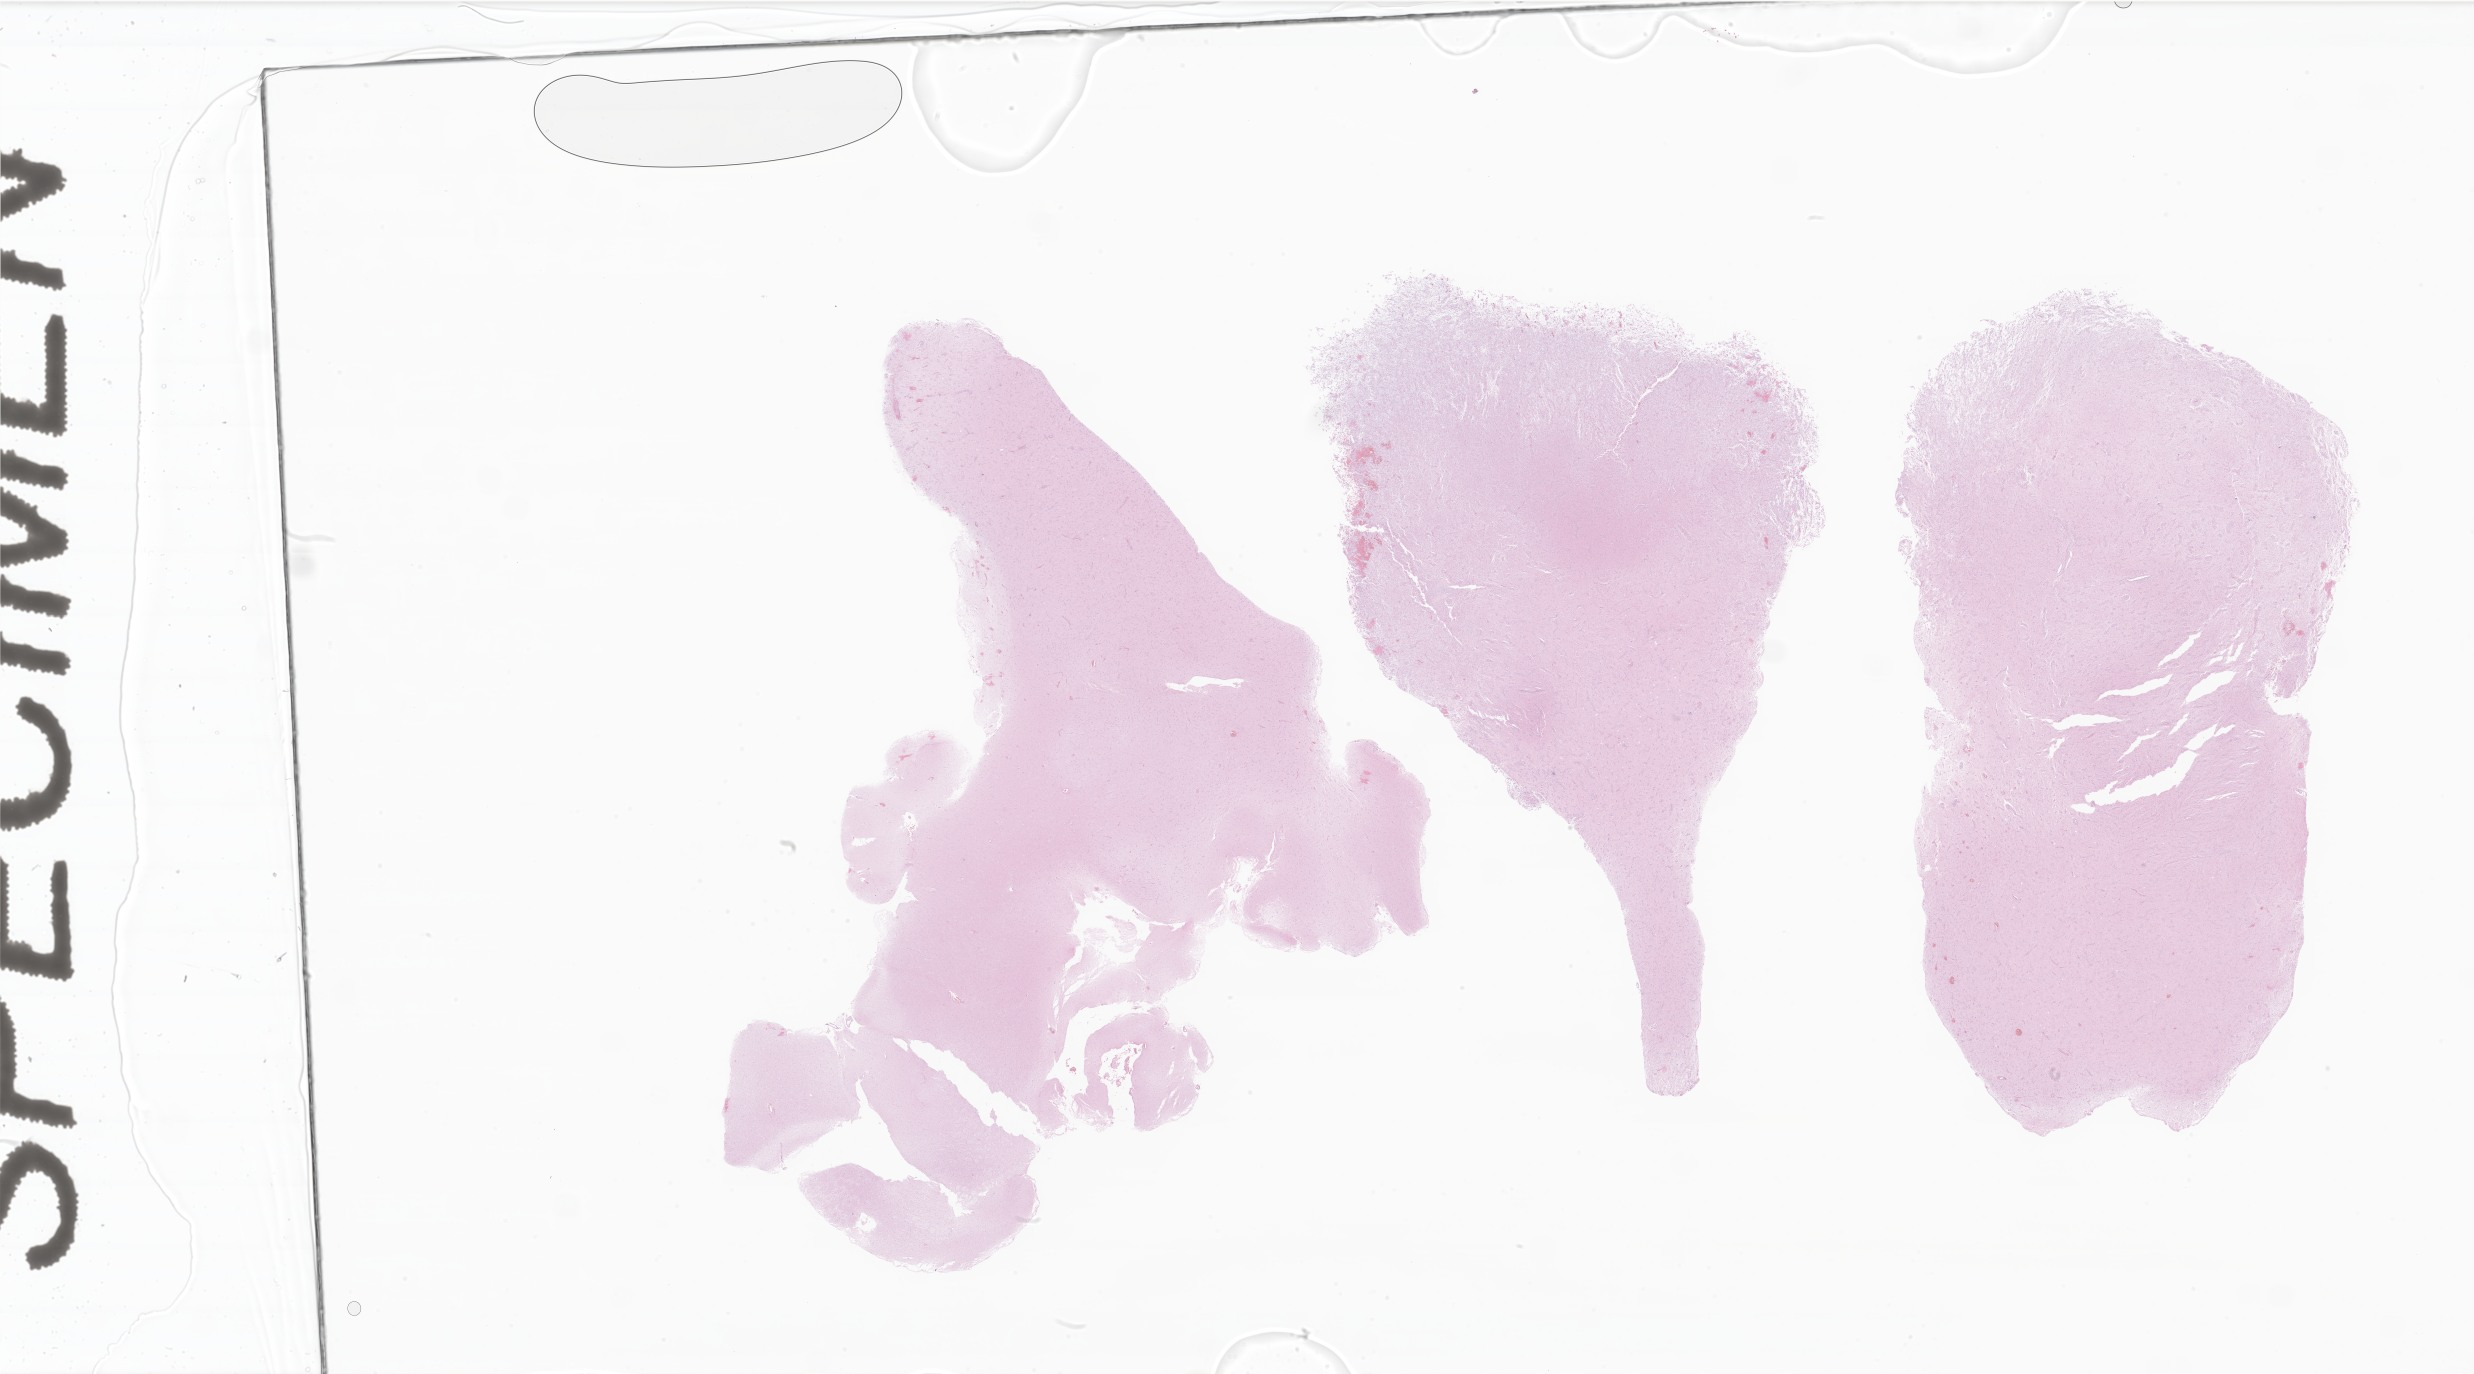
H&E whole-slide image of tumor tissue from the brain, shown as a low-resolution overview of the whole scanned area (about 41.7 x 23.2 mm), formalin-fixed paraffin-embedded section. Patient male; age 35 months (2 years 11 months).
Recorded diagnosis: Glioma, malignant.